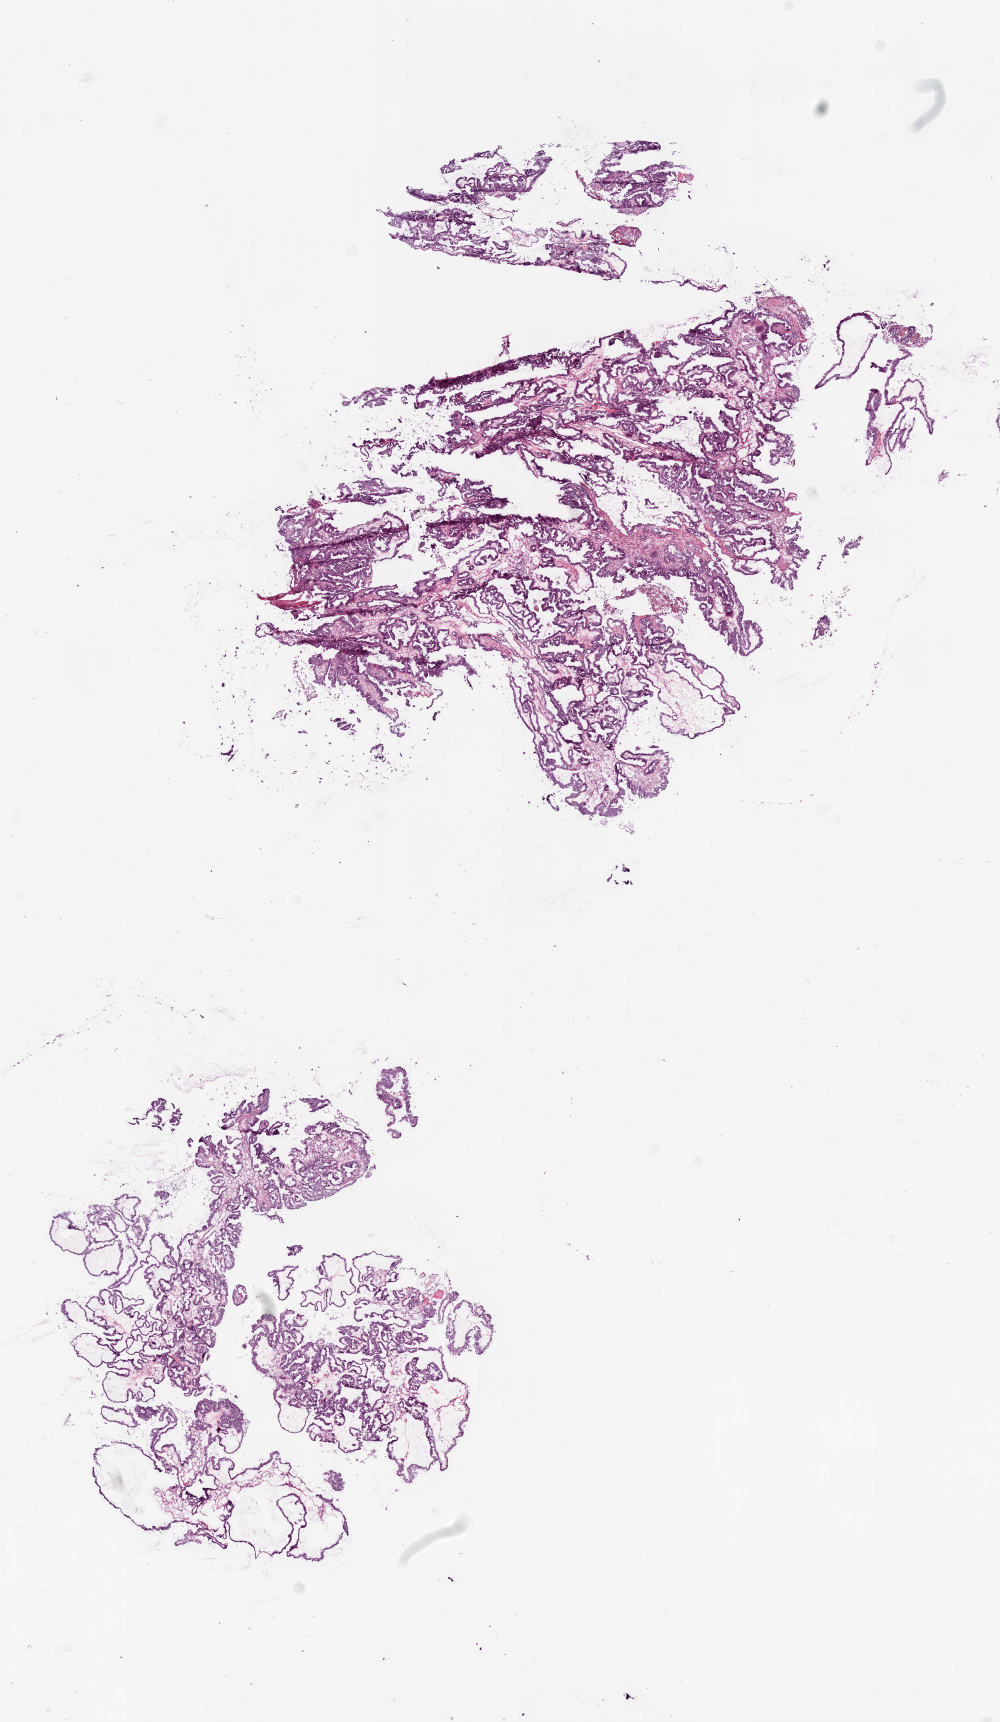
H&E whole-slide image, whole scanned area (about 8.0 x 13.8 mm, slide scanned at 20x) shown as a low-resolution overview; frozen section from the bottom of the tissue portion; sample: primary tumour, ovary. Female patient; age at initial diagnosis 50 years. Histologic grade: G2 (moderately differentiated). Slide review estimates, as recorded: tumour cells 70%, tumour nuclei 90%, normal cells 0%, stromal cells 30%, necrosis 0%.
FIGO stage: IC. Laterality: left. Histologic diagnosis: Serous cystadenocarcinoma, NOS.